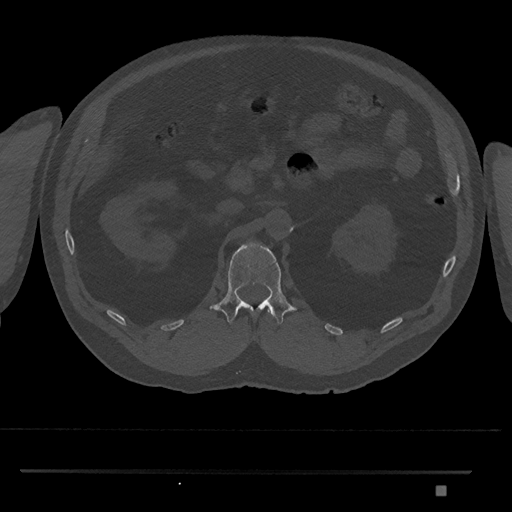
CT including the spine, one axial slice. Position 830 of 1134 along the scan axis. 120 kVp. Bone window (W 1800 / L 400 HU). 0.5 mm slice thickness. 512 × 512 image matrix, field of view 429 × 429 mm. Patient: male, 65 years. Case-level facts recorded for this patient, not image findings: primary cancer: prostate.
Structures marked on this image (semi-automatic segmentation, software-assisted and operator-edited):
- L1 vertebra: bounding box (x1, y1, x2, y2) in pixels: (209, 242, 298, 324)
- T12 vertebra: (269, 312, 272, 315)